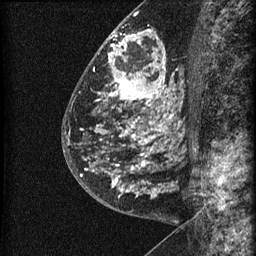
Breast MRI (dynamic contrast-enhanced), one sagittal slice. Position 30 of 60 along the scan axis. Dynamic contrast-enhanced series, image 2 of 3 at this slice position (ordered by acquisition). 1.5 T. TE 4.2 ms, TR 22.7 ms. 1.5 mm slice thickness. 256 × 256 image matrix. Female patient, age 48 years. Case-level facts recorded for this patient, not image findings: setting: breast cancer imaged before/during neoadjuvant chemotherapy; receptor status: triple-negative.
Outlined on this slice (semi-automatic segmentation, software-assisted and operator-edited):
- analysis volume of interest (the breast-tissue region the enhancement analysis was run in; not a lesion): box from (x=81, y=23) to (x=186, y=202) px
- tumour enhancement mask (voxels above the 90 % enhancement threshold inside the analysis volume of interest): (x=81, y=31)–(x=173, y=196)